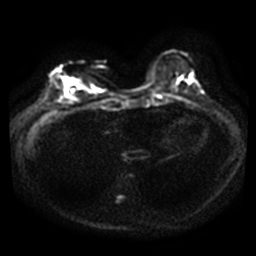
Breast MRI, one axial slice. Slice 10 of 40 in the series (ordered by position). Diffusion-weighted series; image 2 of 4 stored at this slice position (different b-values; order by instance number). 3 T. 5 mm slice thickness. 256 × 256 image matrix. Female patient.
Outlined on this slice (manually delineated by an expert):
- tumour on diffusion-weighted imaging: box from (x=67, y=77) to (x=82, y=90) px